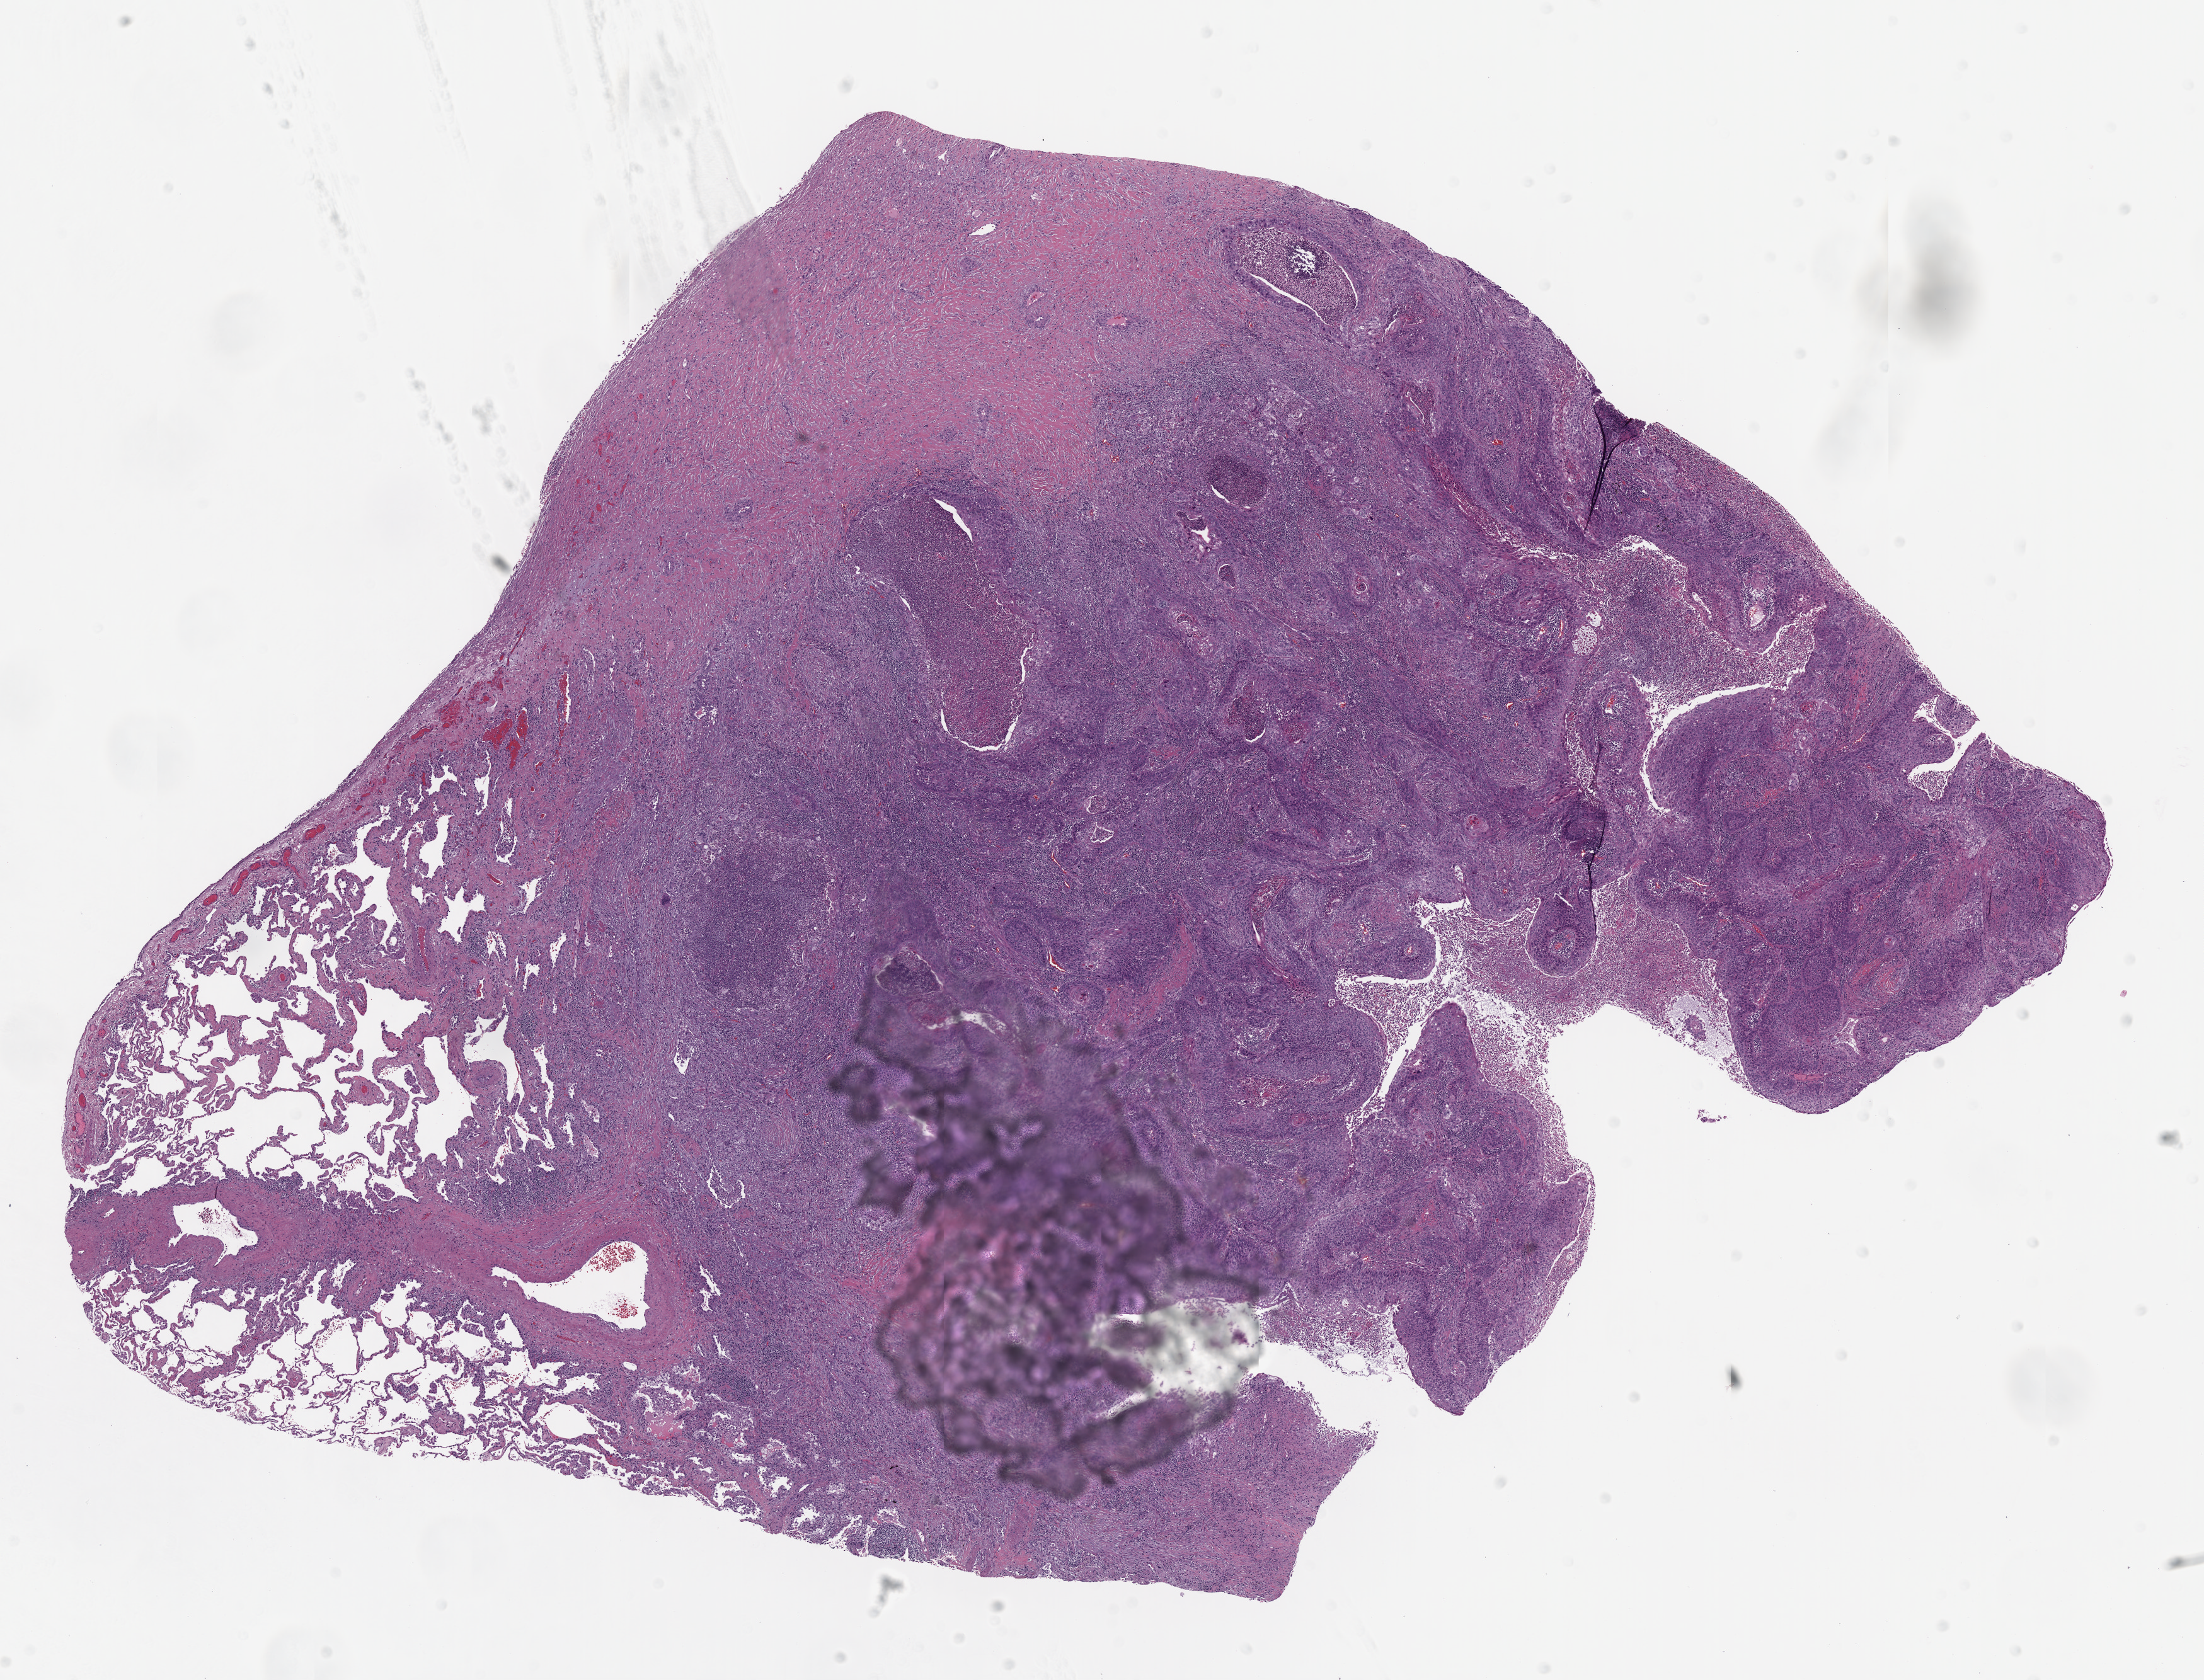
Digitized H&E tissue section (whole slide) — low-resolution overview of the scanned area, about 14.0 x 10.7 mm. FFPE section. Lung, primary tumour sample. Female patient; age at initial diagnosis 70 years.
Pathologic diagnosis: Squamous cell carcinoma, NOS (upper lobe, lung). AJCC pathologic stage: IB (6th edition).